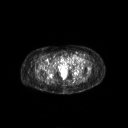
FDG PET of an extremity soft-tissue mass (from a PET/CT study), one axial slice; position 50 of 267 along the scan axis; 3.27 mm slice thickness; 128 × 128 image matrix. Patient: female, 47 years. From the clinical record (not read from this slice): histological type: myxofibrosarcoma; grade: intermediate; site of the primary tumour: left thigh.
Structures marked on this image (expert contour drawn on MRI and transferred to this co-registered scan by the dataset authors):
- gross tumour volume including surrounding oedema: bounding box [x1, y1, x2, y2] px = [66, 55, 83, 63]